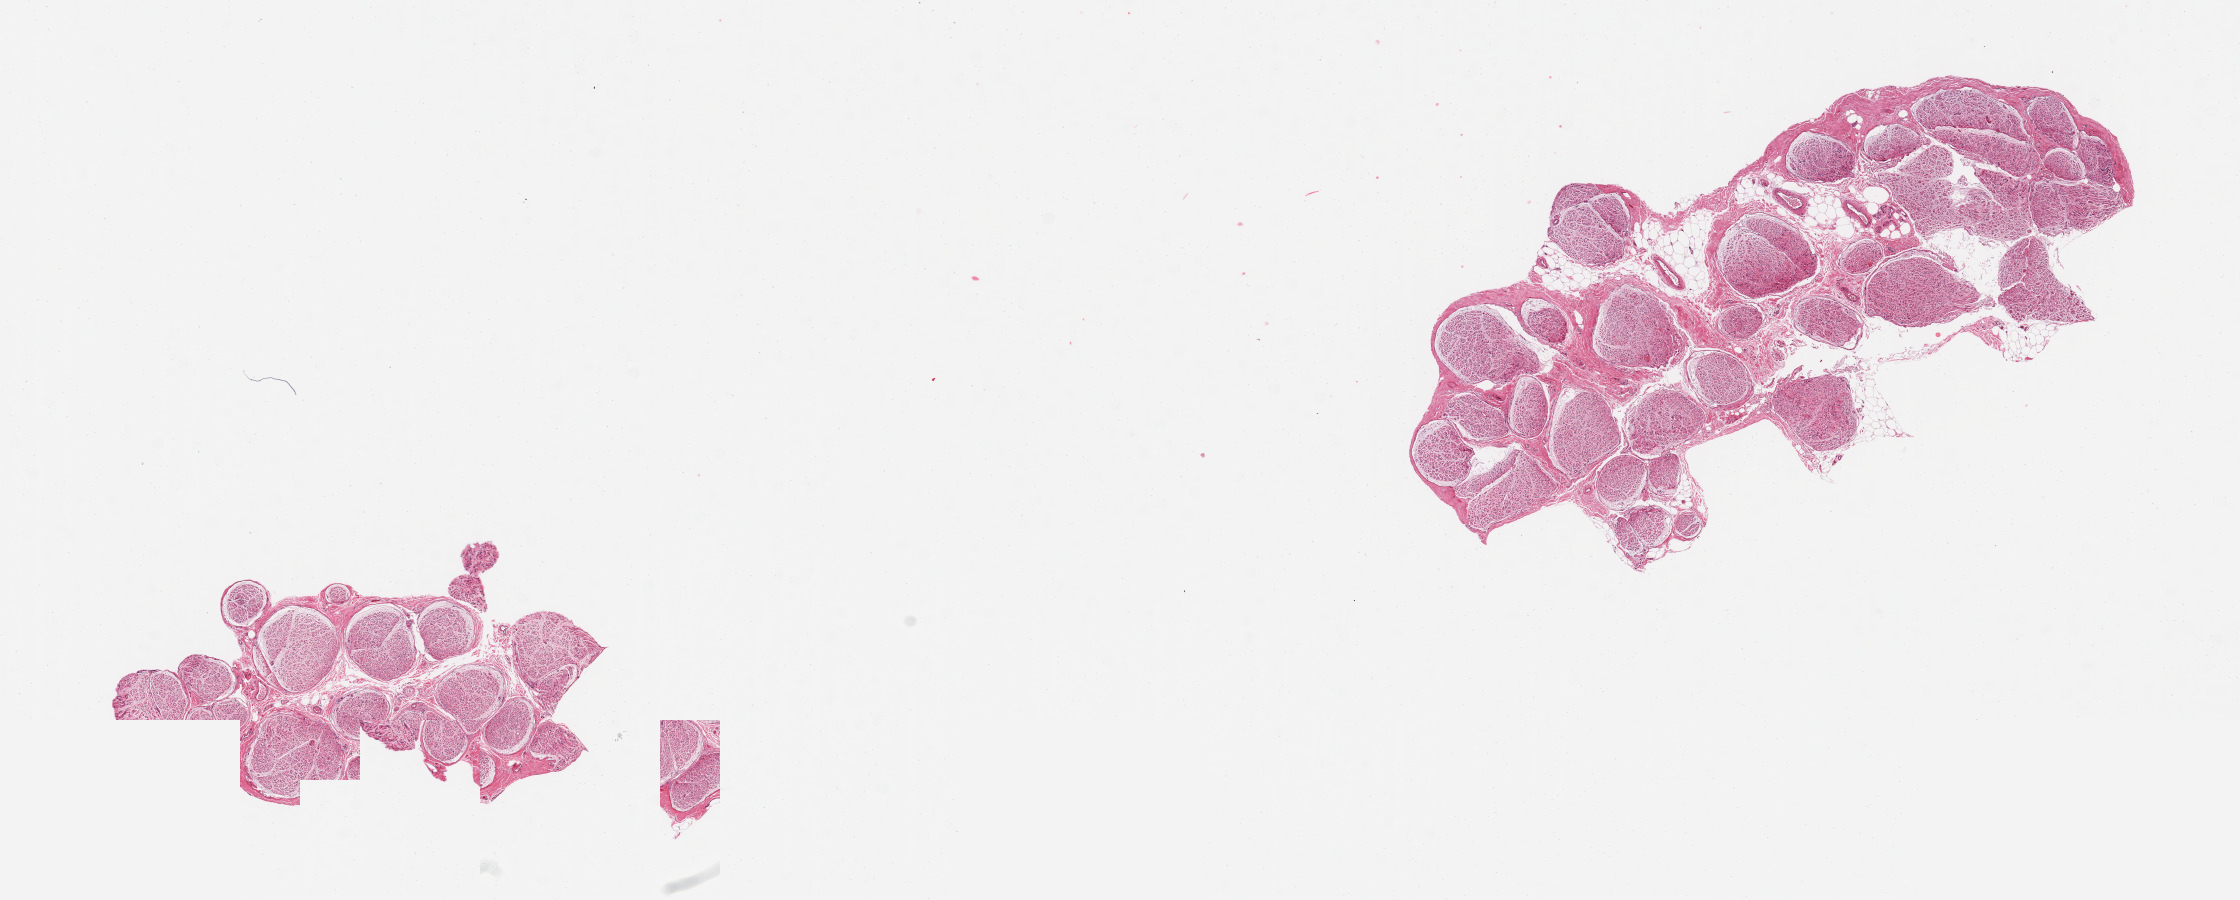
Digitized hematoxylin and eosin (H&E)-stained section, low-resolution overview of the scanned area, about 17.7 x 7.1 mm (slide scanned at 20x). PAXgene-fixed, paraffin-embedded tissue. Section of tibial nerve (target tissue). Donor tissue sample. Donor sex: female.
• reviewer comment on this tissue sample: 2 pieces; 1 piece includes ~10% mostly internal fat